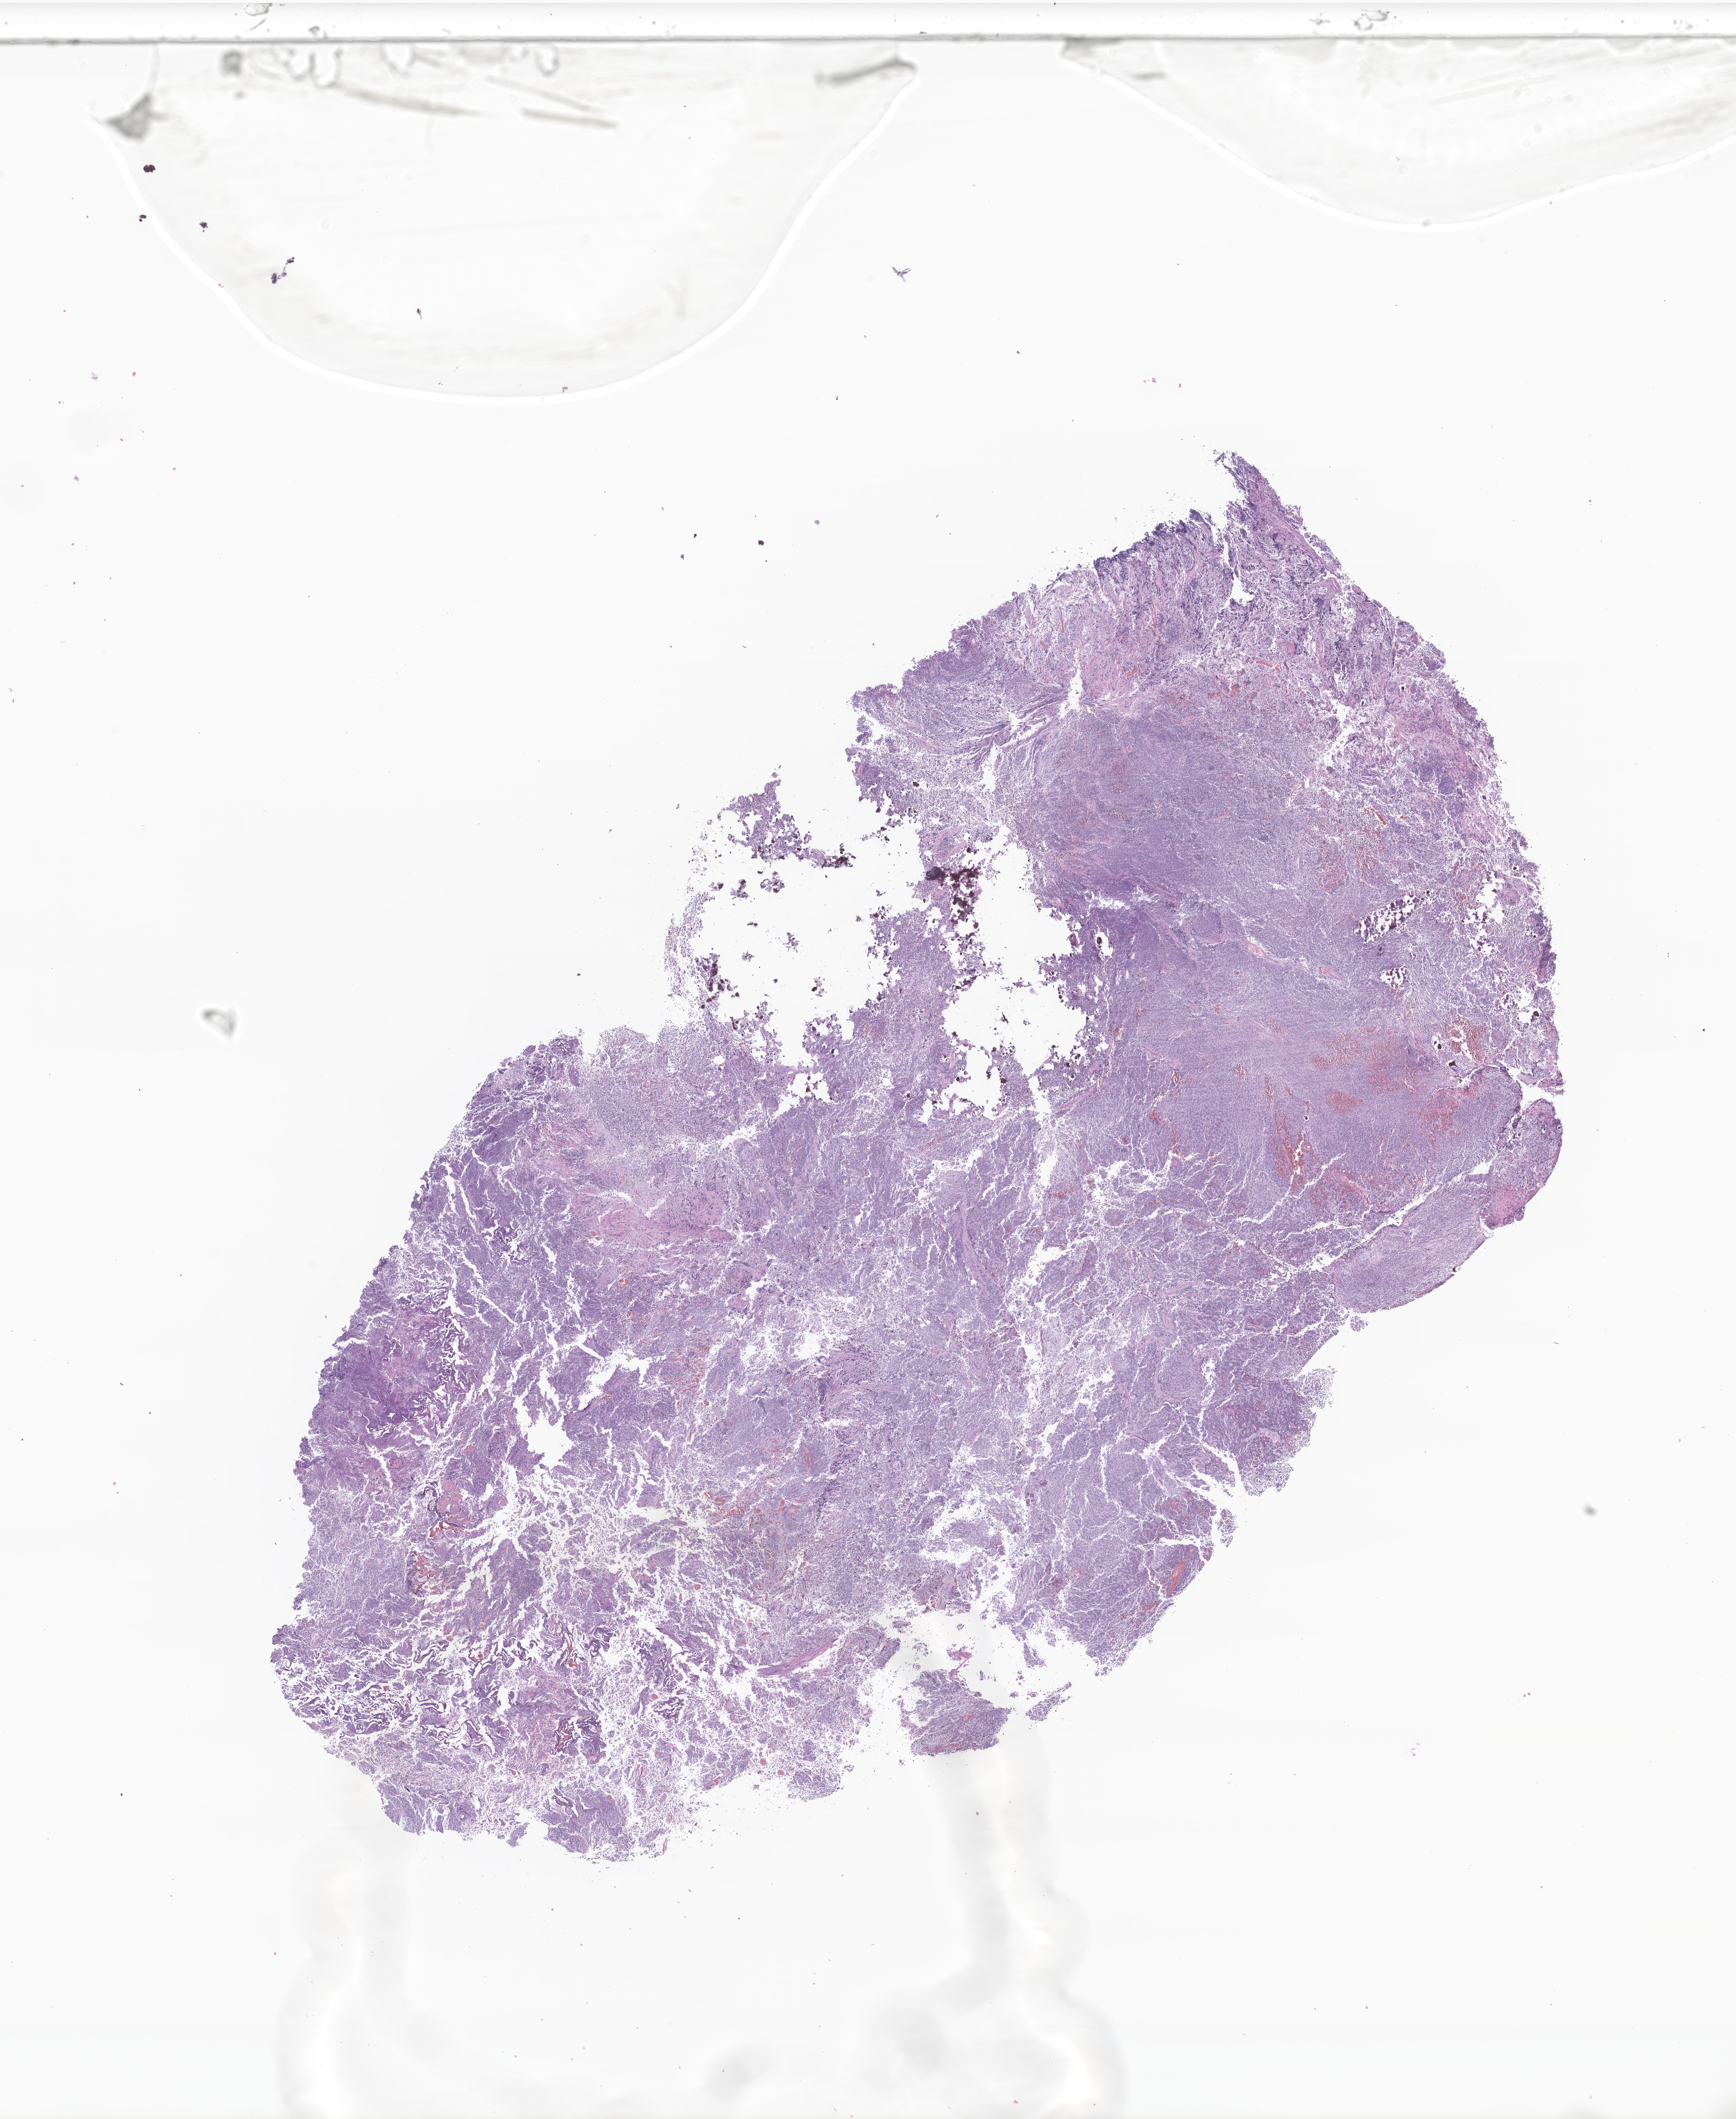
Digitized haematoxylin and eosin-stained section of tumor tissue from the brain — low-resolution overview of the scanned area, about 19.0 x 23.2 mm, formalin-fixed paraffin-embedded section. Patient male; age 79 months (6 years 7 months).
Recorded diagnosis: Medulloblastoma, NOS.